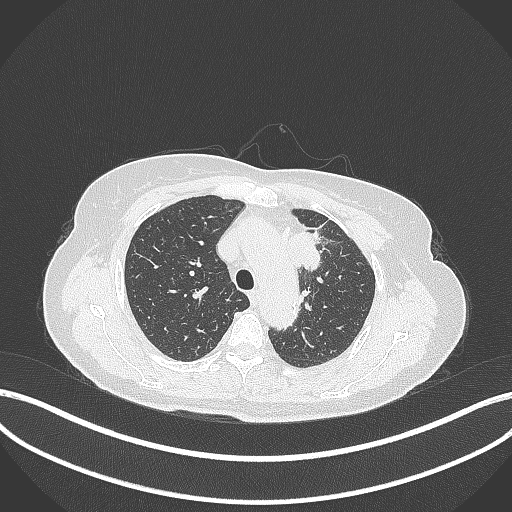
Chest CT, one axial slice. Slice 249 of 369 in the series (ordered by position). Reconstruction kernel B70f. 120 kVp. Lung window (W 1500 / L -600 HU). 1 mm slice thickness. 512 × 512 image matrix, field of view 400 × 400 mm. Female patient, age 65 years. From the clinical record (not read from this slice): clinical TNM (as recorded): T2a N0 M0.
Annotated regions visible in this slice (bounding box drawn by a radiologist):
- lung tumour (recorded histology: adenocarcinoma): box from (x=287, y=228) to (x=325, y=272) px